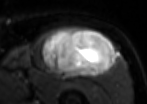
MRI of an extremity soft-tissue mass, one axial slice. Slice 62 of 85 in the series (ordered by position). T2-weighted fat-saturated. MR volume resampled by the dataset authors to the PET/CT grid (not the native acquisition matrix). 3.27 mm slice thickness. 147 × 104 image matrix. Male patient. Case-level facts recorded for this patient, not image findings: histological type: extraskeletal osteosarcoma; grade: high; site of the primary tumour: thigh.
Annotated regions visible in this slice (expert contour drawn on MRI and transferred to this co-registered scan by the dataset authors):
- gross tumour volume (mass): box from (x=40, y=28) to (x=116, y=77) px